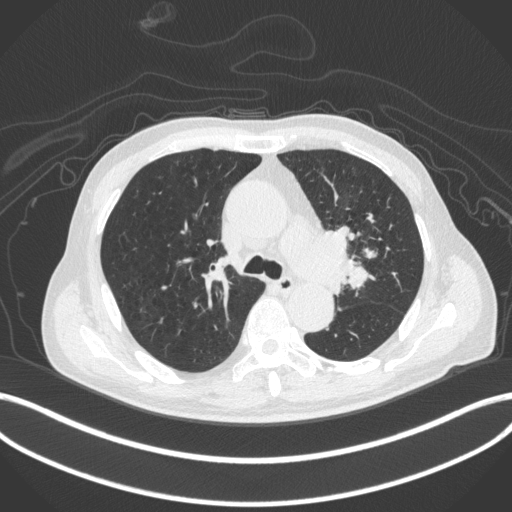
Chest CT, one axial slice; slice 288 of 420 in the series (ordered by position); 120 kVp; lung window (W 1500 / L -600 HU); 512 × 512 image matrix. Patient: male, 77 years. From the clinical record (not read from this slice): clinical TNM (as recorded): T3 N1 M0.
Outlined on this slice (bounding box drawn by a radiologist):
- lung tumour (recorded histology: adenocarcinoma): box from (x=307, y=223) to (x=365, y=293) px